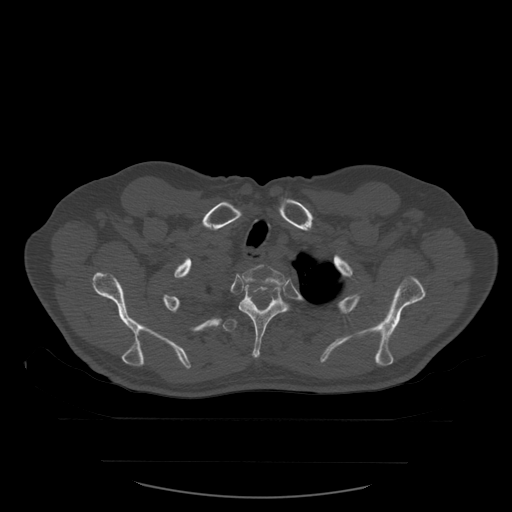
CT including the spine, one axial slice. Slice 459 of 590 in the series (ordered by position). Bone window (W 1800 / L 400 HU). 1.25 mm slice thickness. 512 × 512 image matrix. Patient age 71 years. Case-level facts recorded for this patient, not image findings: primary cancer: lung; vertebrae with lytic lesions (as recorded): T1, T2, L5, S1.
Structures marked on this image (semi-automatically segmented with operator editing):
- T2 vertebra: bounding box <242,265,285,289> (left, top, right, bottom; pixels)
- T3 vertebra: <238,285,299,358>
- T4 vertebra: <223,300,276,333>